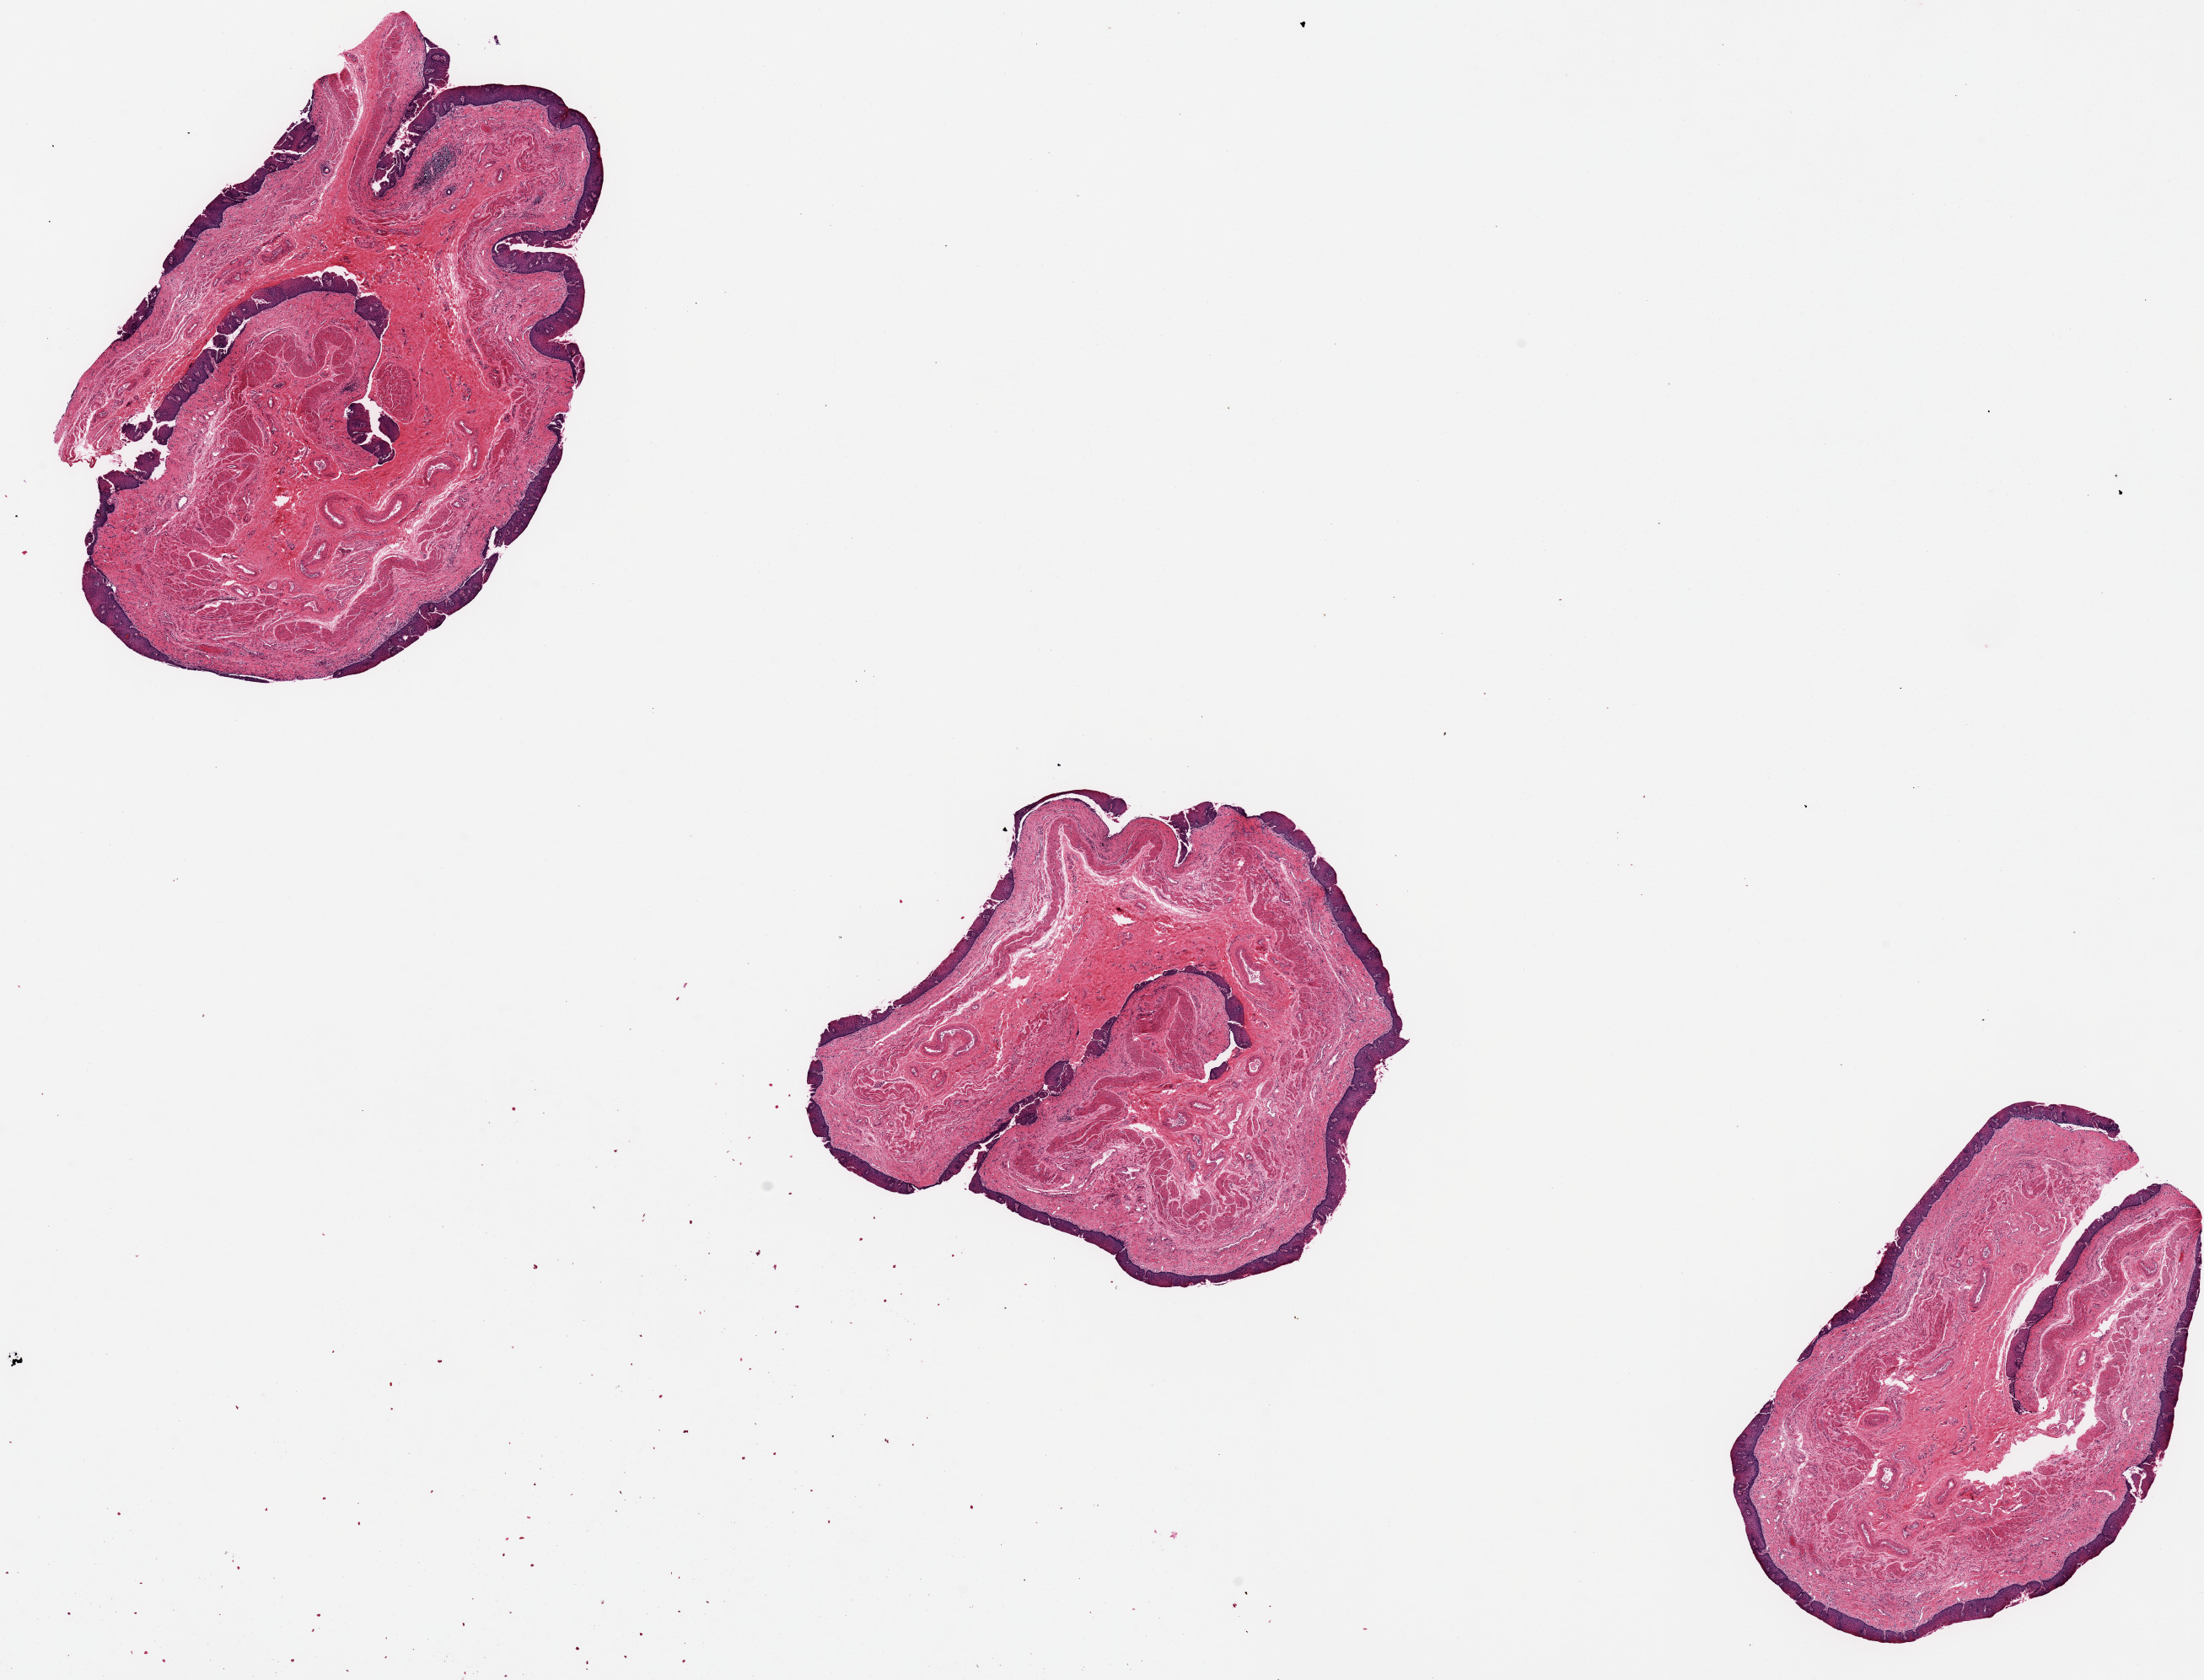
Hematoxylin and eosin (H&E) whole-slide image — a low-resolution overview of the entire scanned area, about 20.7 x 15.8 mm (slide scanned at 20x), PAXgene-fixed, paraffin-embedded tissue, section of esophageal mucous membrane (target tissue), tissue donor sample. Donor sex: female.
* pathologist's review note for this sample: Mucosa present; approximately 7-9% total specimen thickness